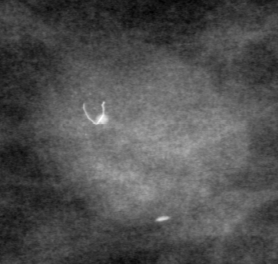
Cropped region of a digitized screen-film mammogram centred on a radiologist-marked abnormality, right breast, CC view, BI-RADS breast density category 2 (scale 1–4).
Mass, shape oval, margins circumscribed; BI-RADS assessment category 3; pathology result (as recorded, not read from the image): benign.